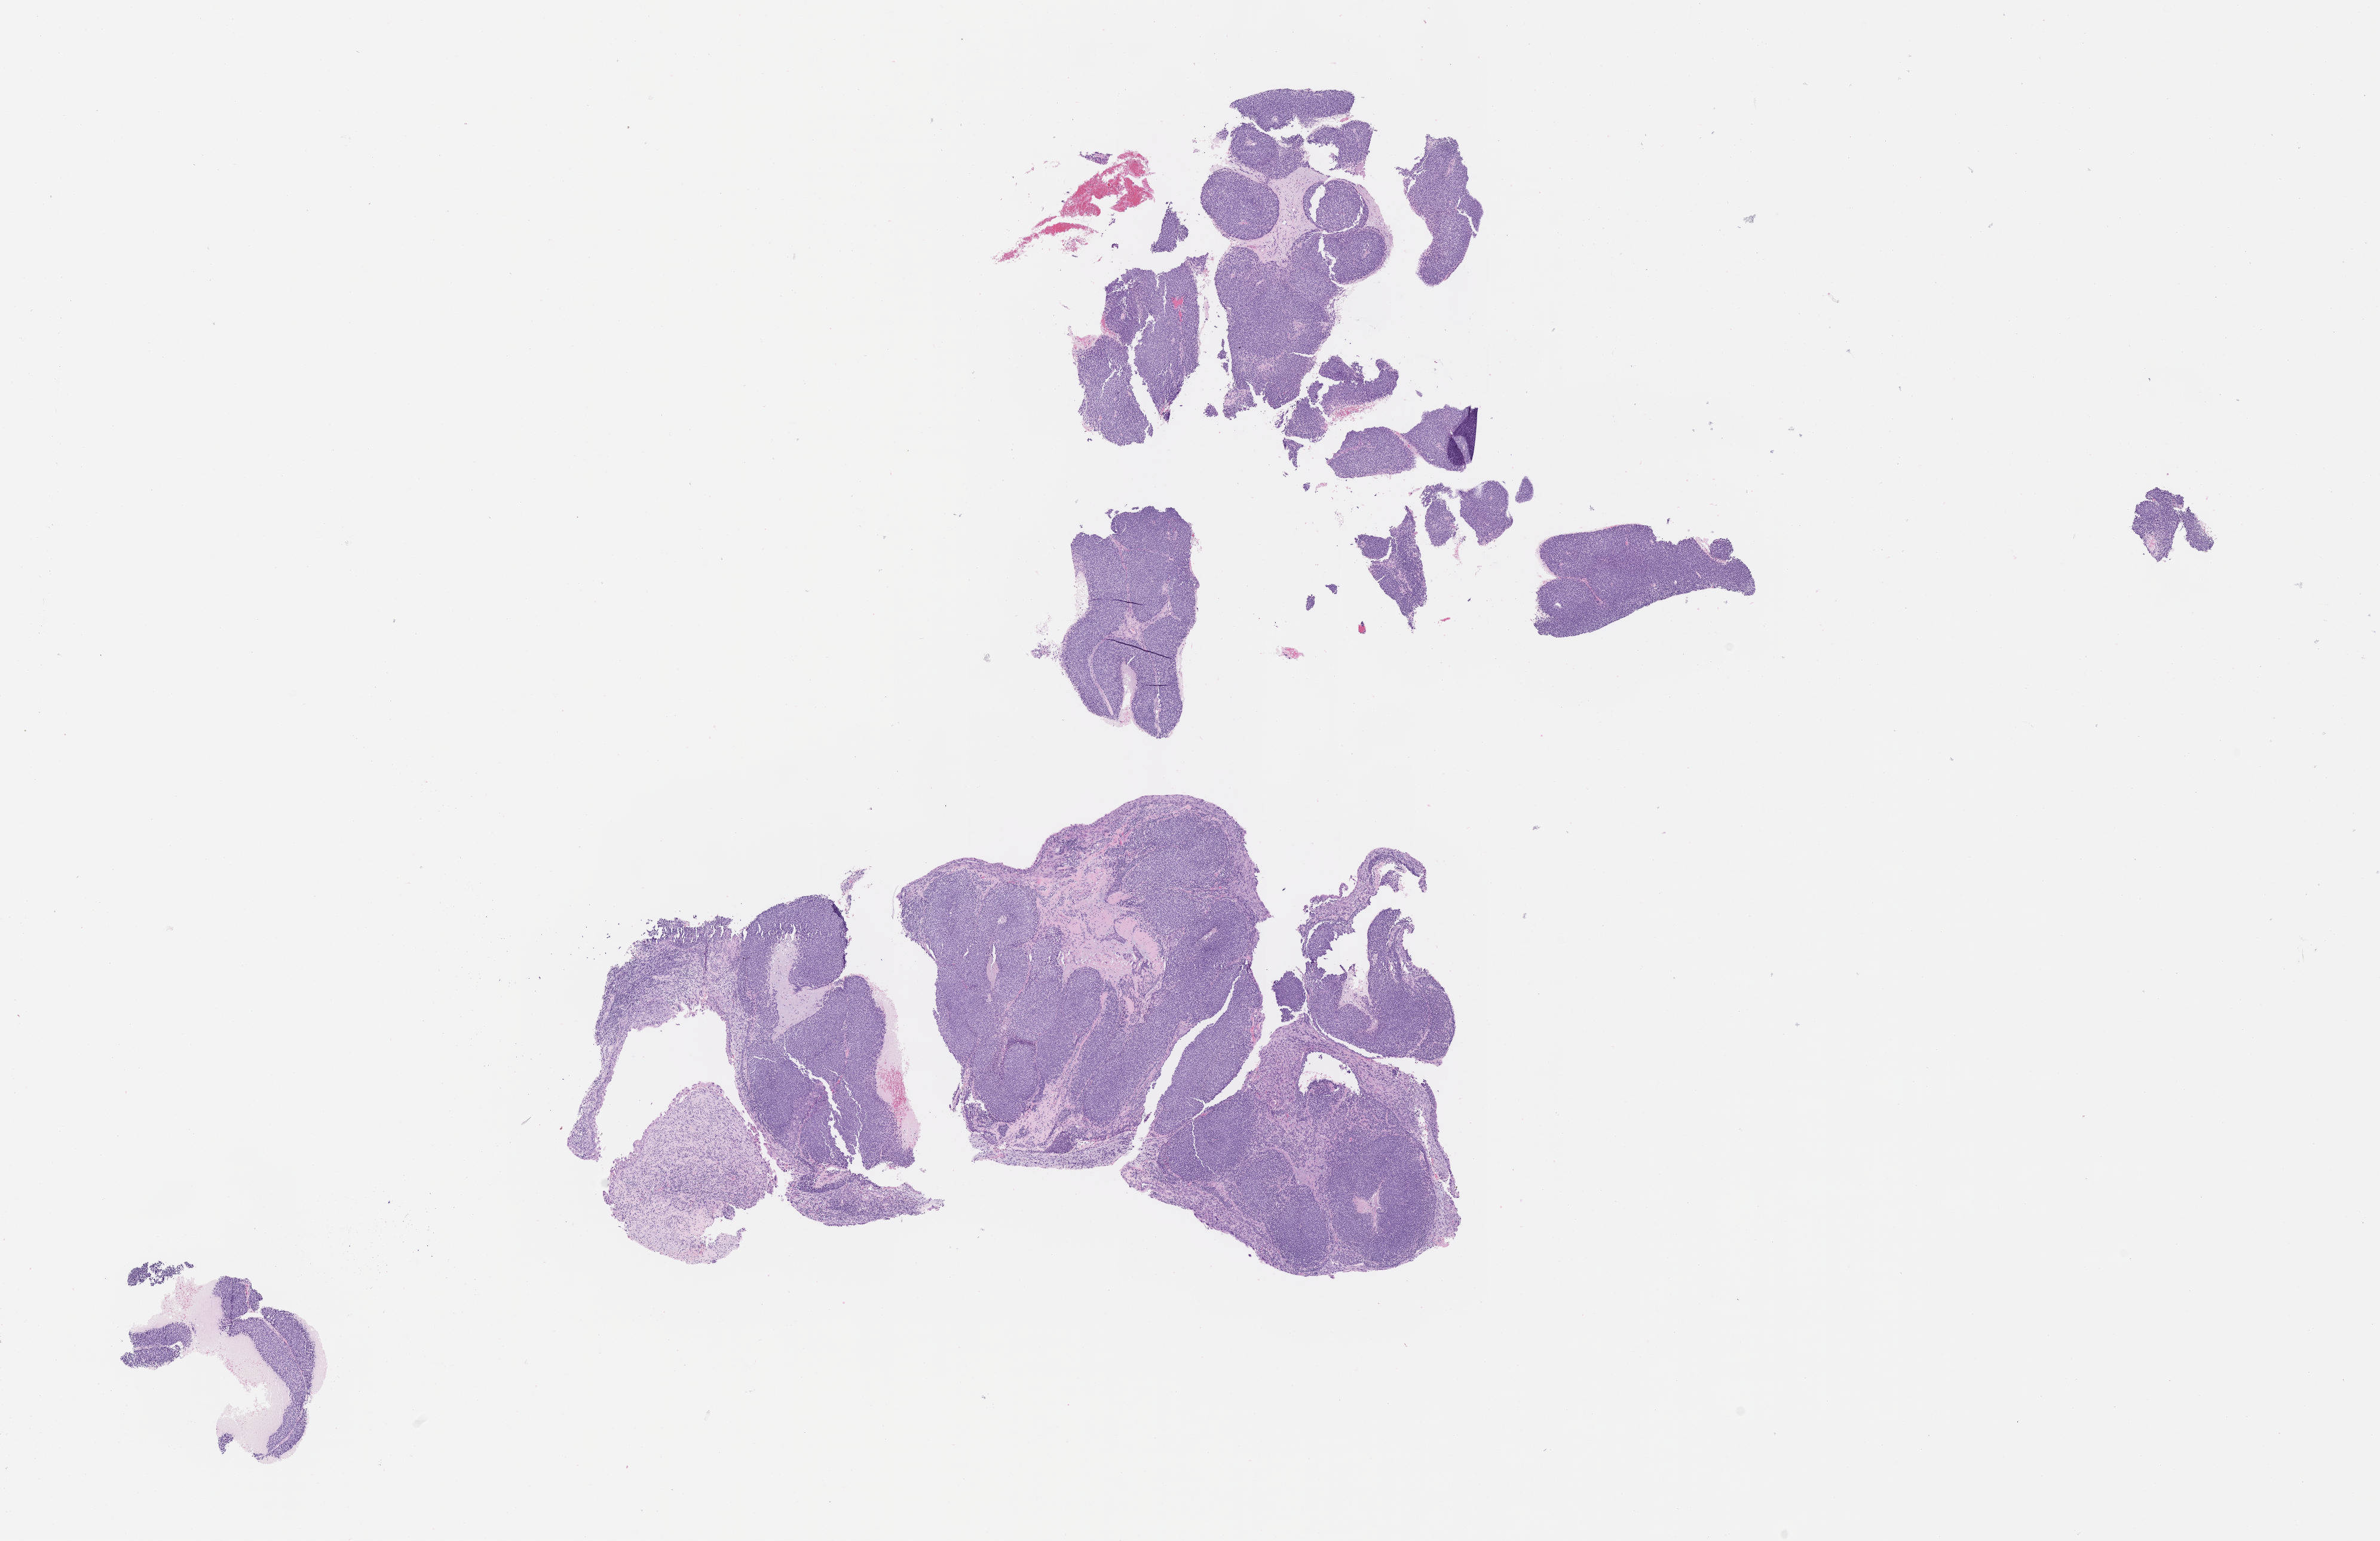
Whole-slide image, H&E stain, shown as a low-resolution overview of the whole scanned area (about 16.1 x 10.4 mm); specimen: tumor tissue; anatomic site: cervix. Female patient, 71 years old.
* diagnosis: Squamous cell carcinoma, large cell, nonkeratinizing, NOS